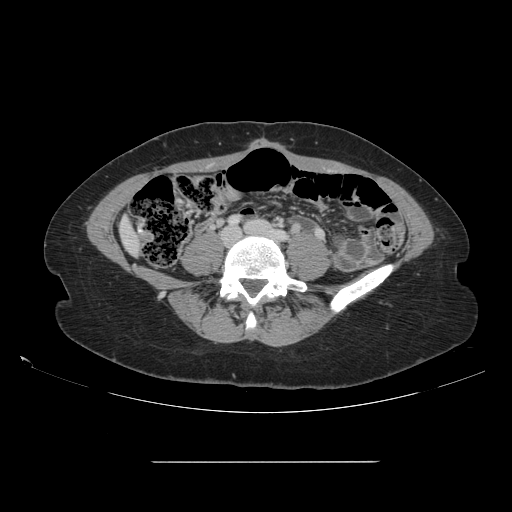
Contrast-enhanced abdominal CT, one axial slice. Position 8 of 151 along the scan axis. 120 kVp. Intravenous contrast given. Soft-tissue window (W 400 / L 40 HU). 512 × 512 image matrix. Female patient, age 46 years. Case-level facts recorded for this patient, not image findings: diagnosis: colorectal cancer liver metastases, imaged before liver resection; multiple liver metastases: yes; largest metastasis: 3 cm; chemotherapy before resection: no.
Structures marked on this image (expert manual segmentation):
- liver: box from (x=121, y=222) to (x=140, y=253) px
- planned liver remnant (the part of the liver to remain after resection): (x=121, y=222)–(x=140, y=253)